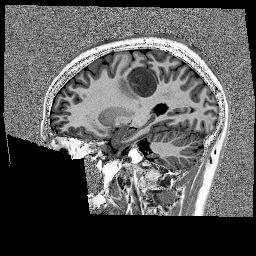
Brain MRI from a brain-tumour surgery series, one sagittal slice; slice 66 of 176 in the series (ordered by position); 1 mm slice thickness; 256 × 256 image matrix, field of view 256 × 256 mm. From the clinical record (not read from this slice): histopathology: Glioblastoma; WHO grade: 4; IDH mutation: no.
Annotated regions visible in this slice (manually delineated by an expert):
- tumour: box from (x=118, y=60) to (x=175, y=93) px